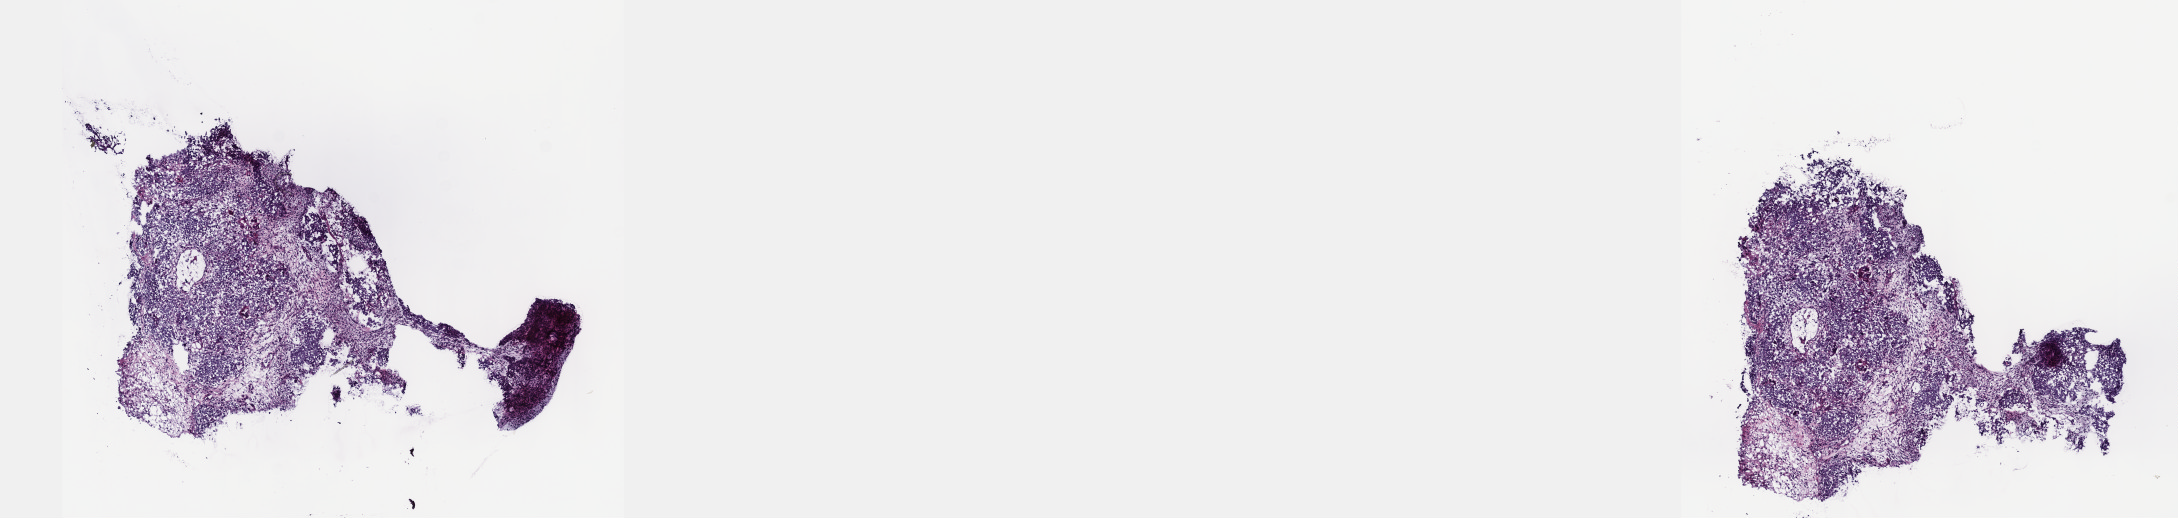
Digitized H&E tissue section (whole slide) — whole scanned area (about 17.6 x 4.2 mm, acquisition: 40x scan) shown as a low-resolution overview; frozen section from the top of the tissue portion; primary tumour sample from the testis. Male, age 24 years at initial diagnosis. Slide review estimates, as recorded: tumour cells 90%, tumour nuclei 90%, normal cells 0%, stromal cells 10%, necrosis 0%. Infiltration values recorded for this section: lymphocyte infiltration 0%, monocyte infiltration 0%, neutrophil infiltration 0%.
• TNM: T2 NX M0
• diagnosis: Embryonal carcinoma, NOS
• AJCC pathologic stage: IS